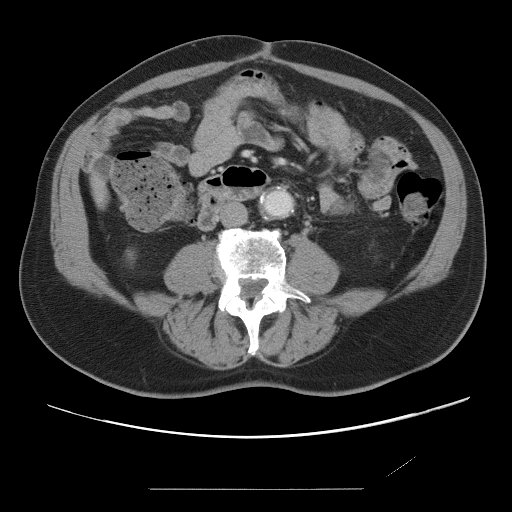
Contrast-enhanced abdominal CT, one axial slice. 120 kVp. Soft-tissue window (W 400 / L 40 HU). 5 mm slice thickness. 512 × 512 image matrix, field of view 406 × 406 mm. Male patient, age 74 years. From the clinical record (not read from this slice): diagnosis: colorectal cancer liver metastases, imaged before liver resection; multiple liver metastases: yes; largest metastasis: 1.1 cm.
Annotated regions visible in this slice (expert manual segmentation):
- liver: box from (x=97, y=188) to (x=102, y=196) px